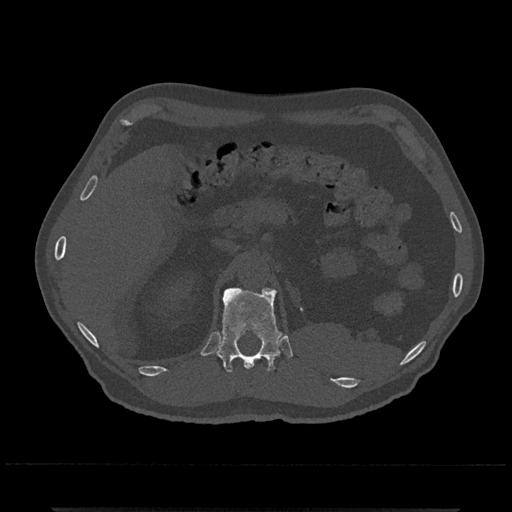
CT including the spine, one axial slice; position 434 of 797 along the scan axis; 120 kVp; bone window (W 1800 / L 400 HU); 512 × 512 image matrix. Male patient, age 67 years. From the clinical record (not read from this slice): primary cancer: prostate.
Structures marked on this image (semi-automatically segmented with operator editing):
- T12 vertebra: bounding box (x1, y1, x2, y2) in pixels: (216, 287, 281, 372)